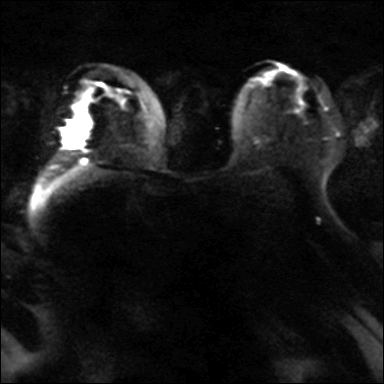
Breast MRI, one axial slice. Slice 23 of 42 in the series (ordered by position). Diffusion-weighted series; image 2 of 4 stored at this slice position (different b-values; order by instance number). 3 T. 4 mm slice thickness. 384 × 384 image matrix. Female patient.
Outlined on this slice (manually delineated by an expert):
- tumour on diffusion-weighted imaging: bounding box <67,122,82,147> (left, top, right, bottom; pixels)